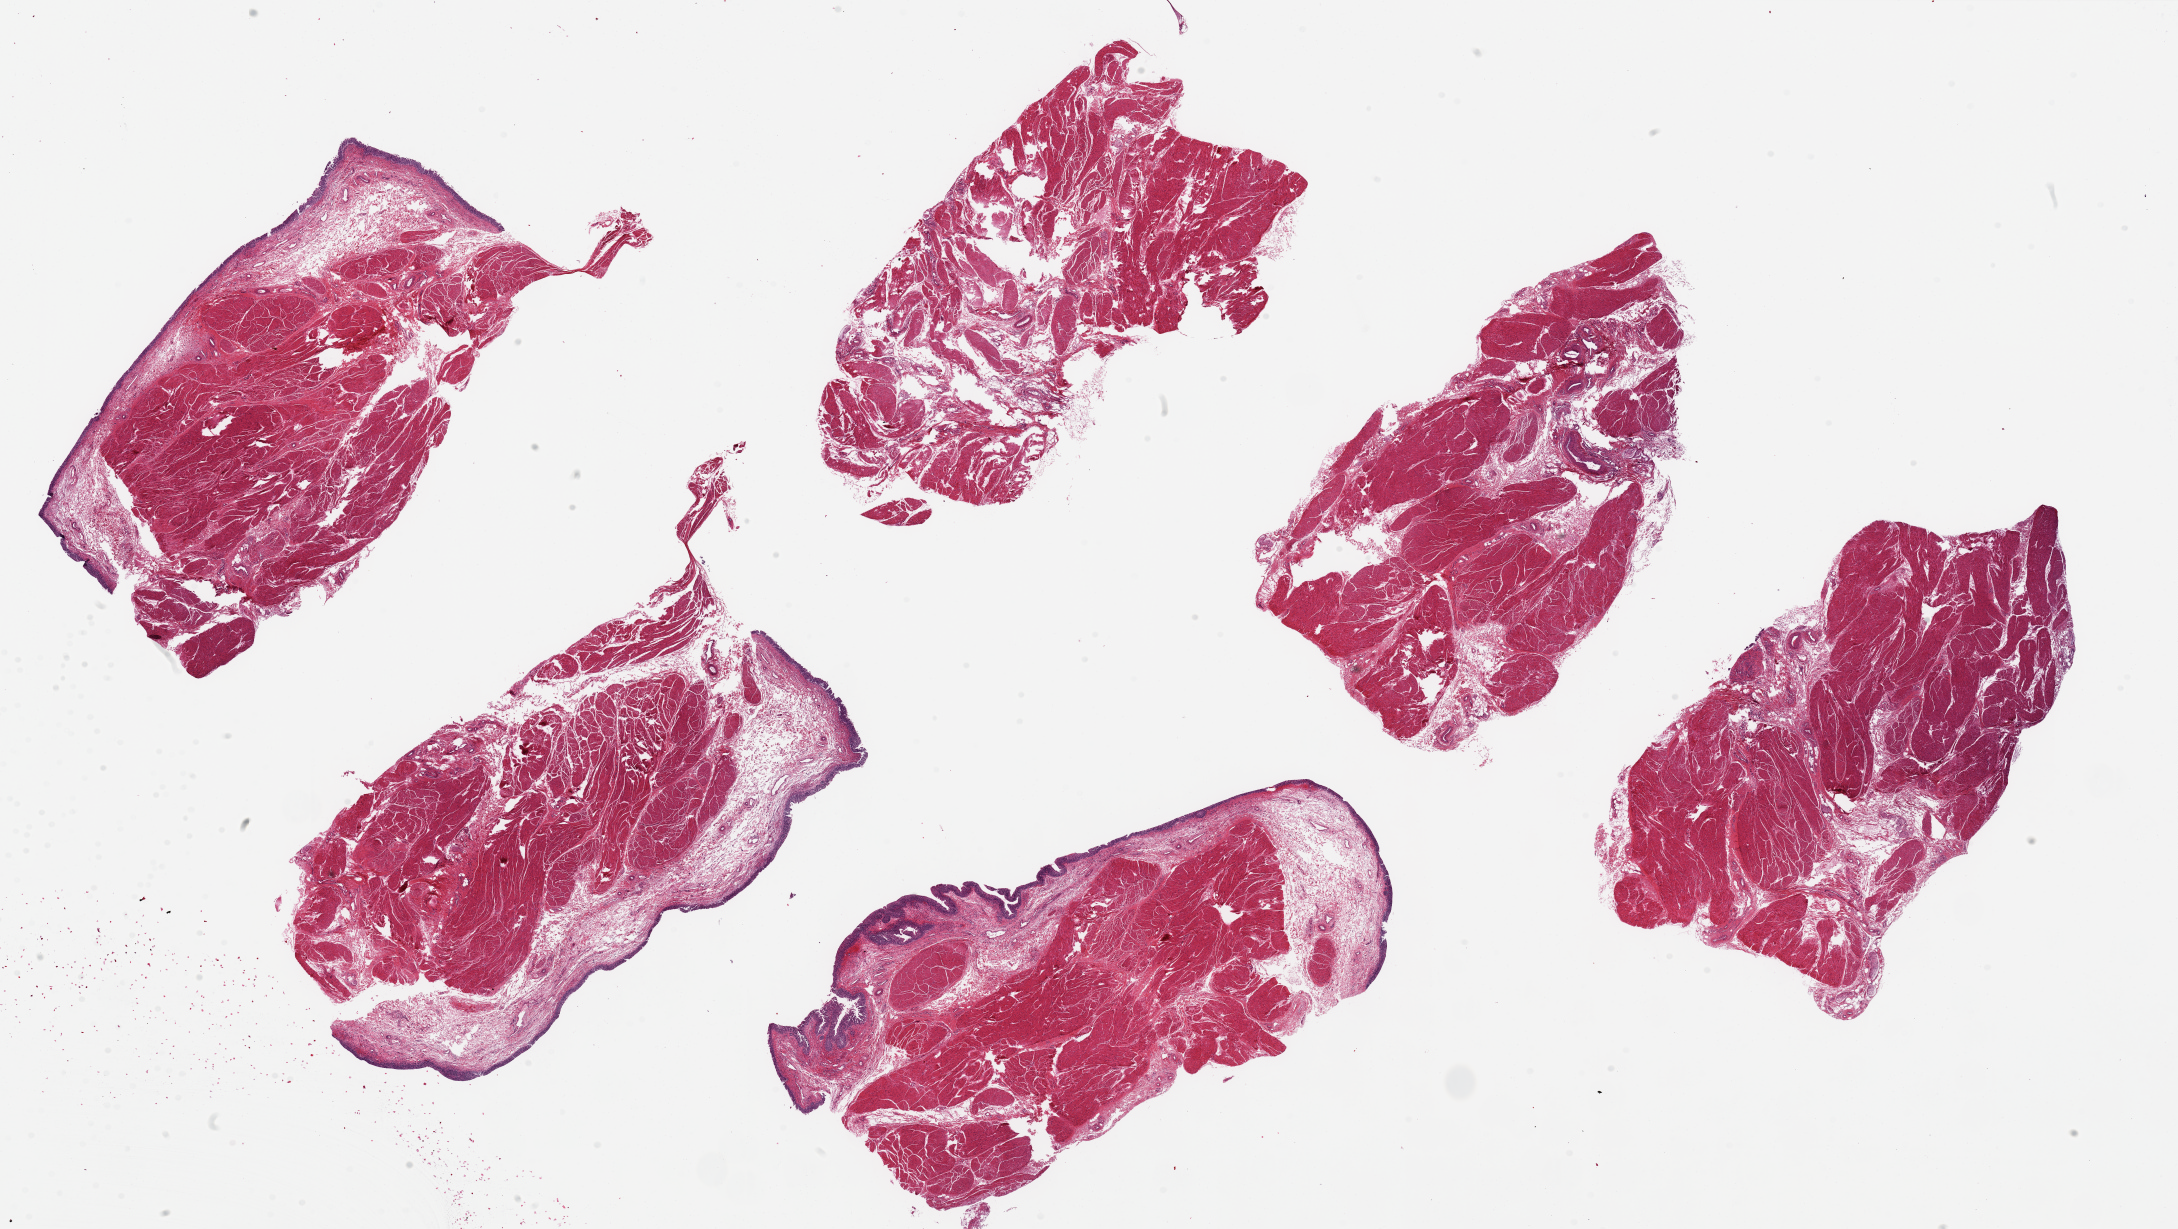
Whole-slide image, haematoxylin and eosin stain — whole scanned area (about 34.5 x 19.4 mm, acquisition: 20x scan) shown as a low-resolution overview; PAXgene-fixed, paraffin-embedded tissue; sampled site (target tissue): urinary bladder; tissue donor sample. Donor sex: male.
* reviewer comment on this tissue sample: 6 ~10x4.8mm pieces. Well preserved epithelium in 3 pieces; none in other 3. Moderate submucosal edema. Moderate fixation artifacts